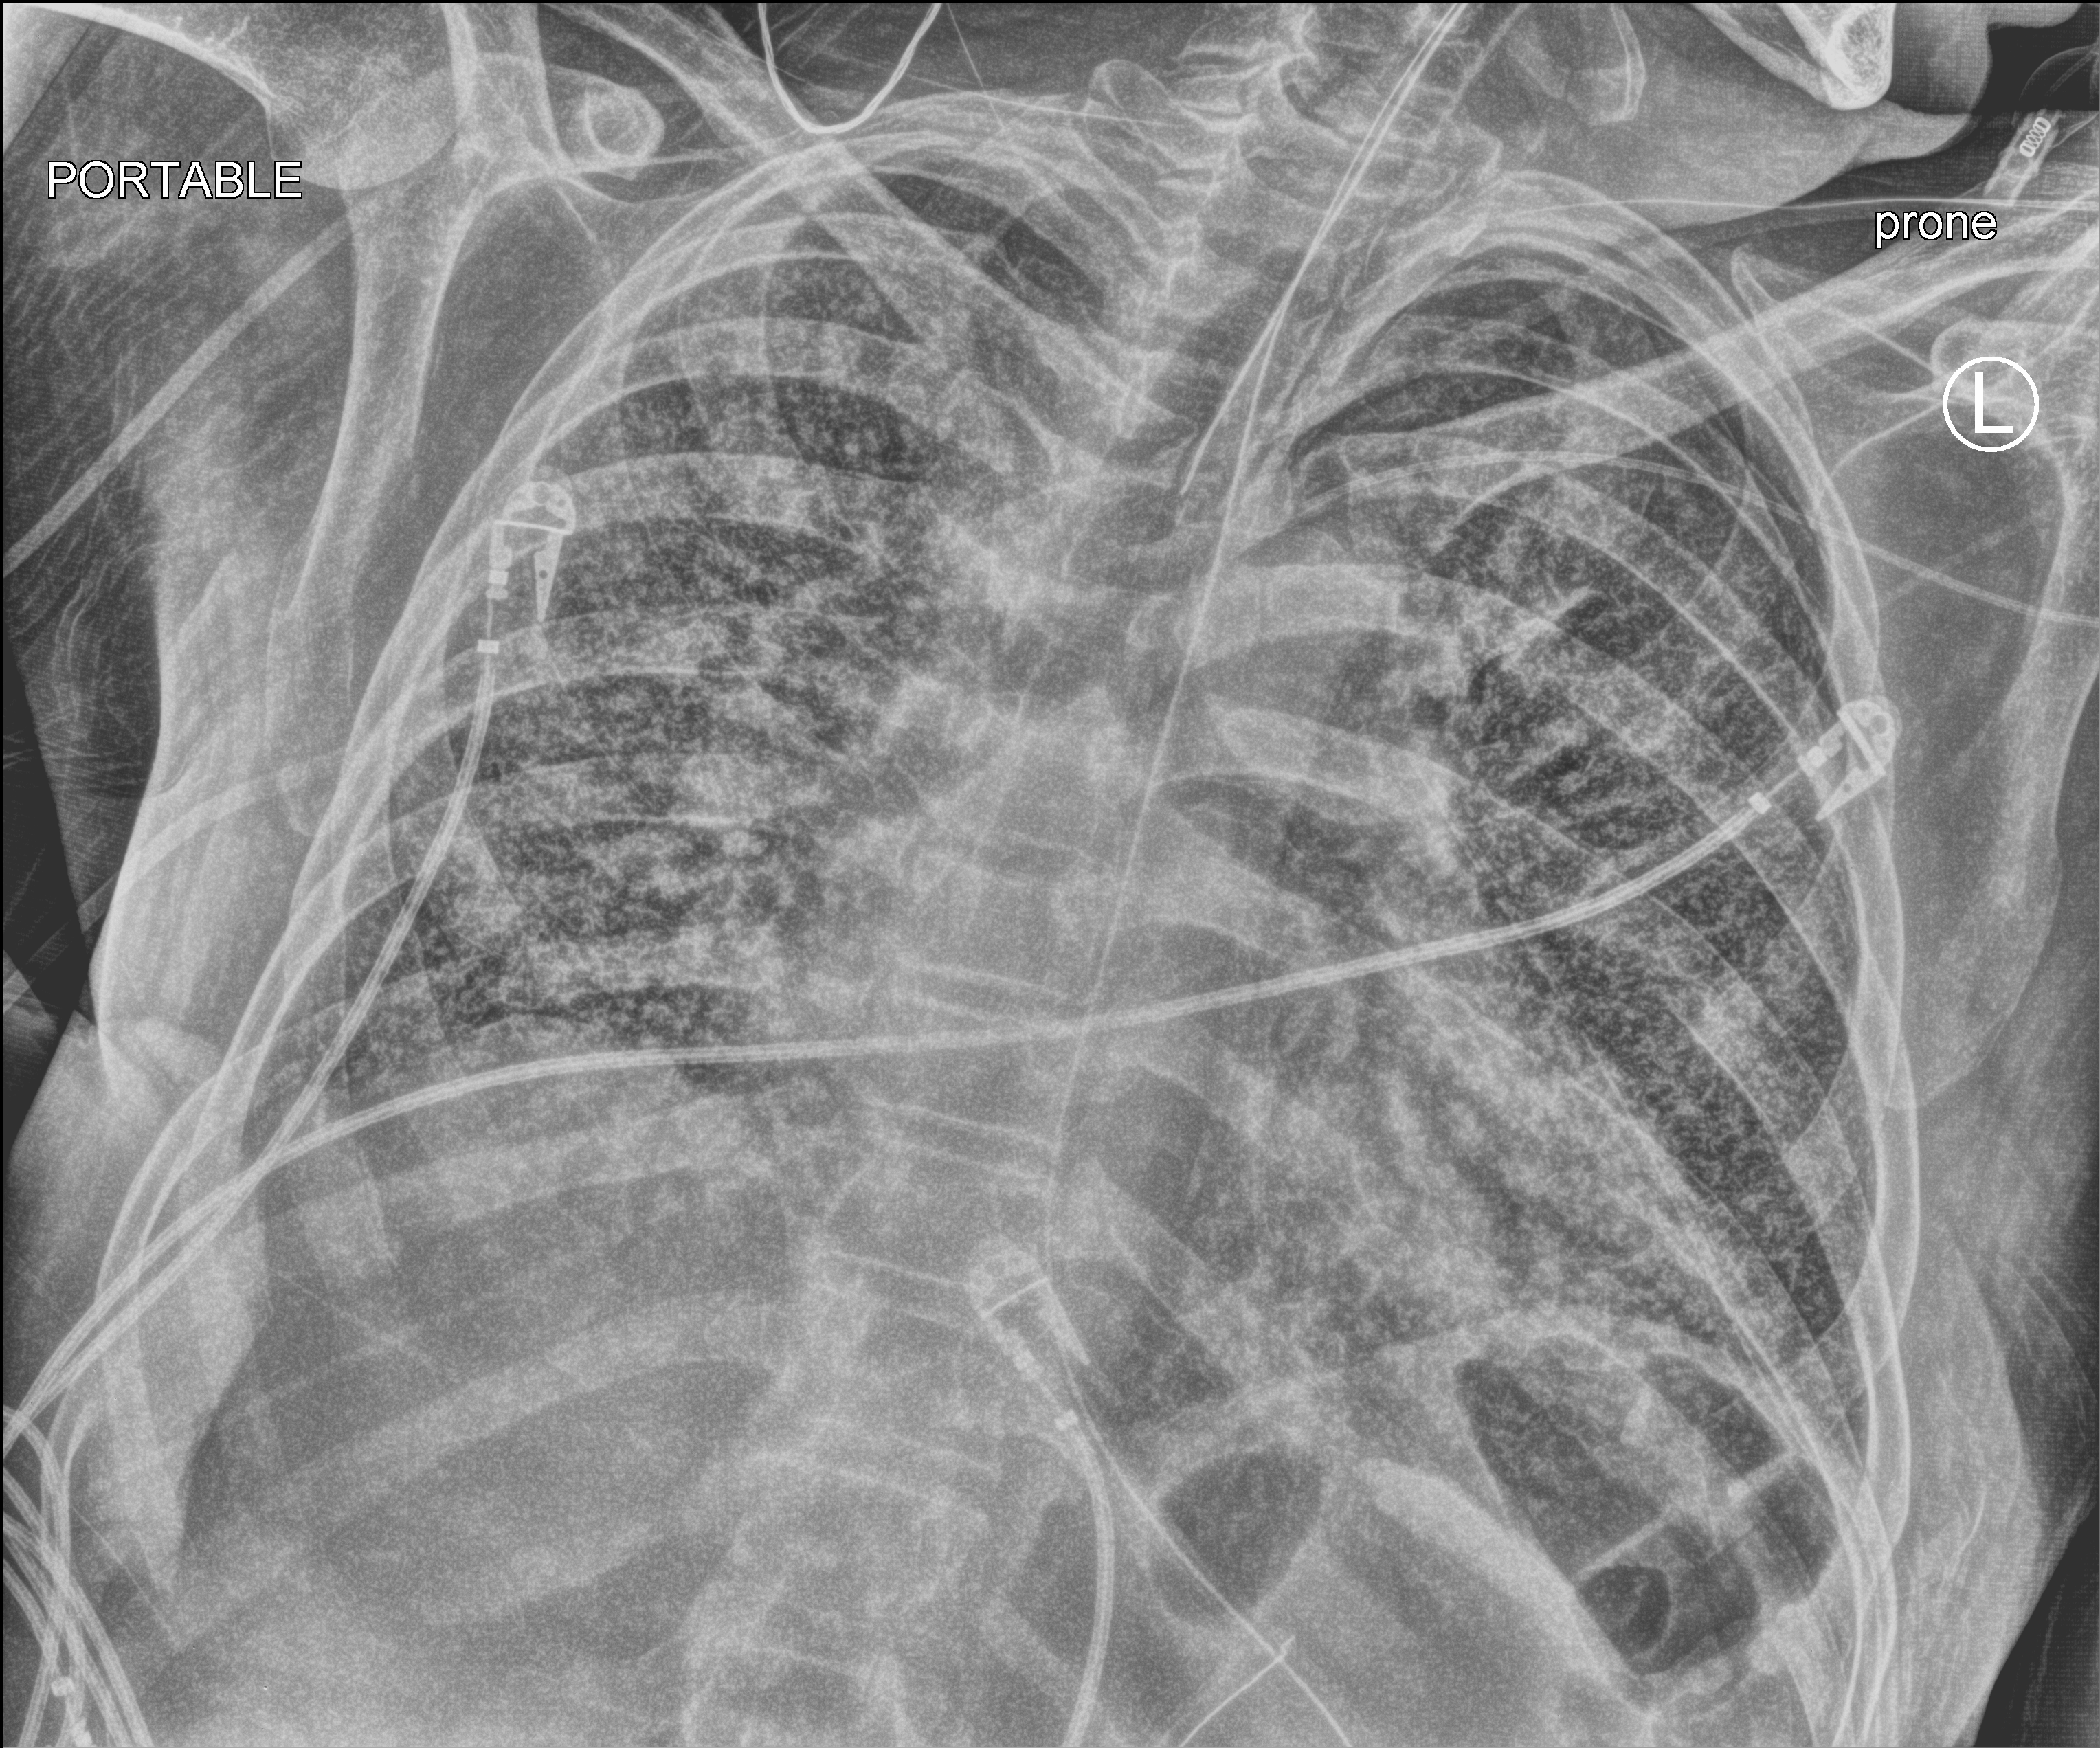
Portable chest radiograph, anteroposterior (AP) projection. Patient hospitalised with COVID-19; male, aged 60–74 years.
Hospital-stay facts (about this admission, not read from this image; timing relative to this image not recorded): mechanically ventilated during this hospital stay: yes; admitted to intensive care during this hospital stay: yes.